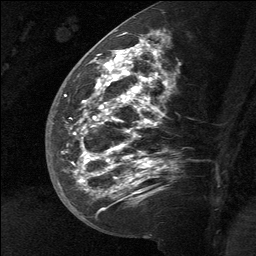
Breast MRI (dynamic contrast-enhanced), one sagittal slice. Dynamic contrast-enhanced study with each time point stored as its own series, time point 2 of 3 at this slice position (early post-contrast, ordered by acquisition time). 1.5 T. TE 4.8 ms, TR 27 ms. 256 × 256 image matrix, field of view 180 × 180 mm. Female patient, age 39 years. Case-level facts recorded for this patient, not image findings: setting: breast cancer imaged before/during neoadjuvant chemotherapy; receptor status: HER2-positive.
Annotated regions visible in this slice (semi-automatically segmented with operator editing):
- analysis volume of interest (the breast-tissue region the enhancement analysis was run in; not a lesion): box from (x=58, y=40) to (x=169, y=217) px
- tumour enhancement mask (voxels above the 90 % enhancement threshold inside the analysis volume of interest): (x=65, y=40)–(x=155, y=193)